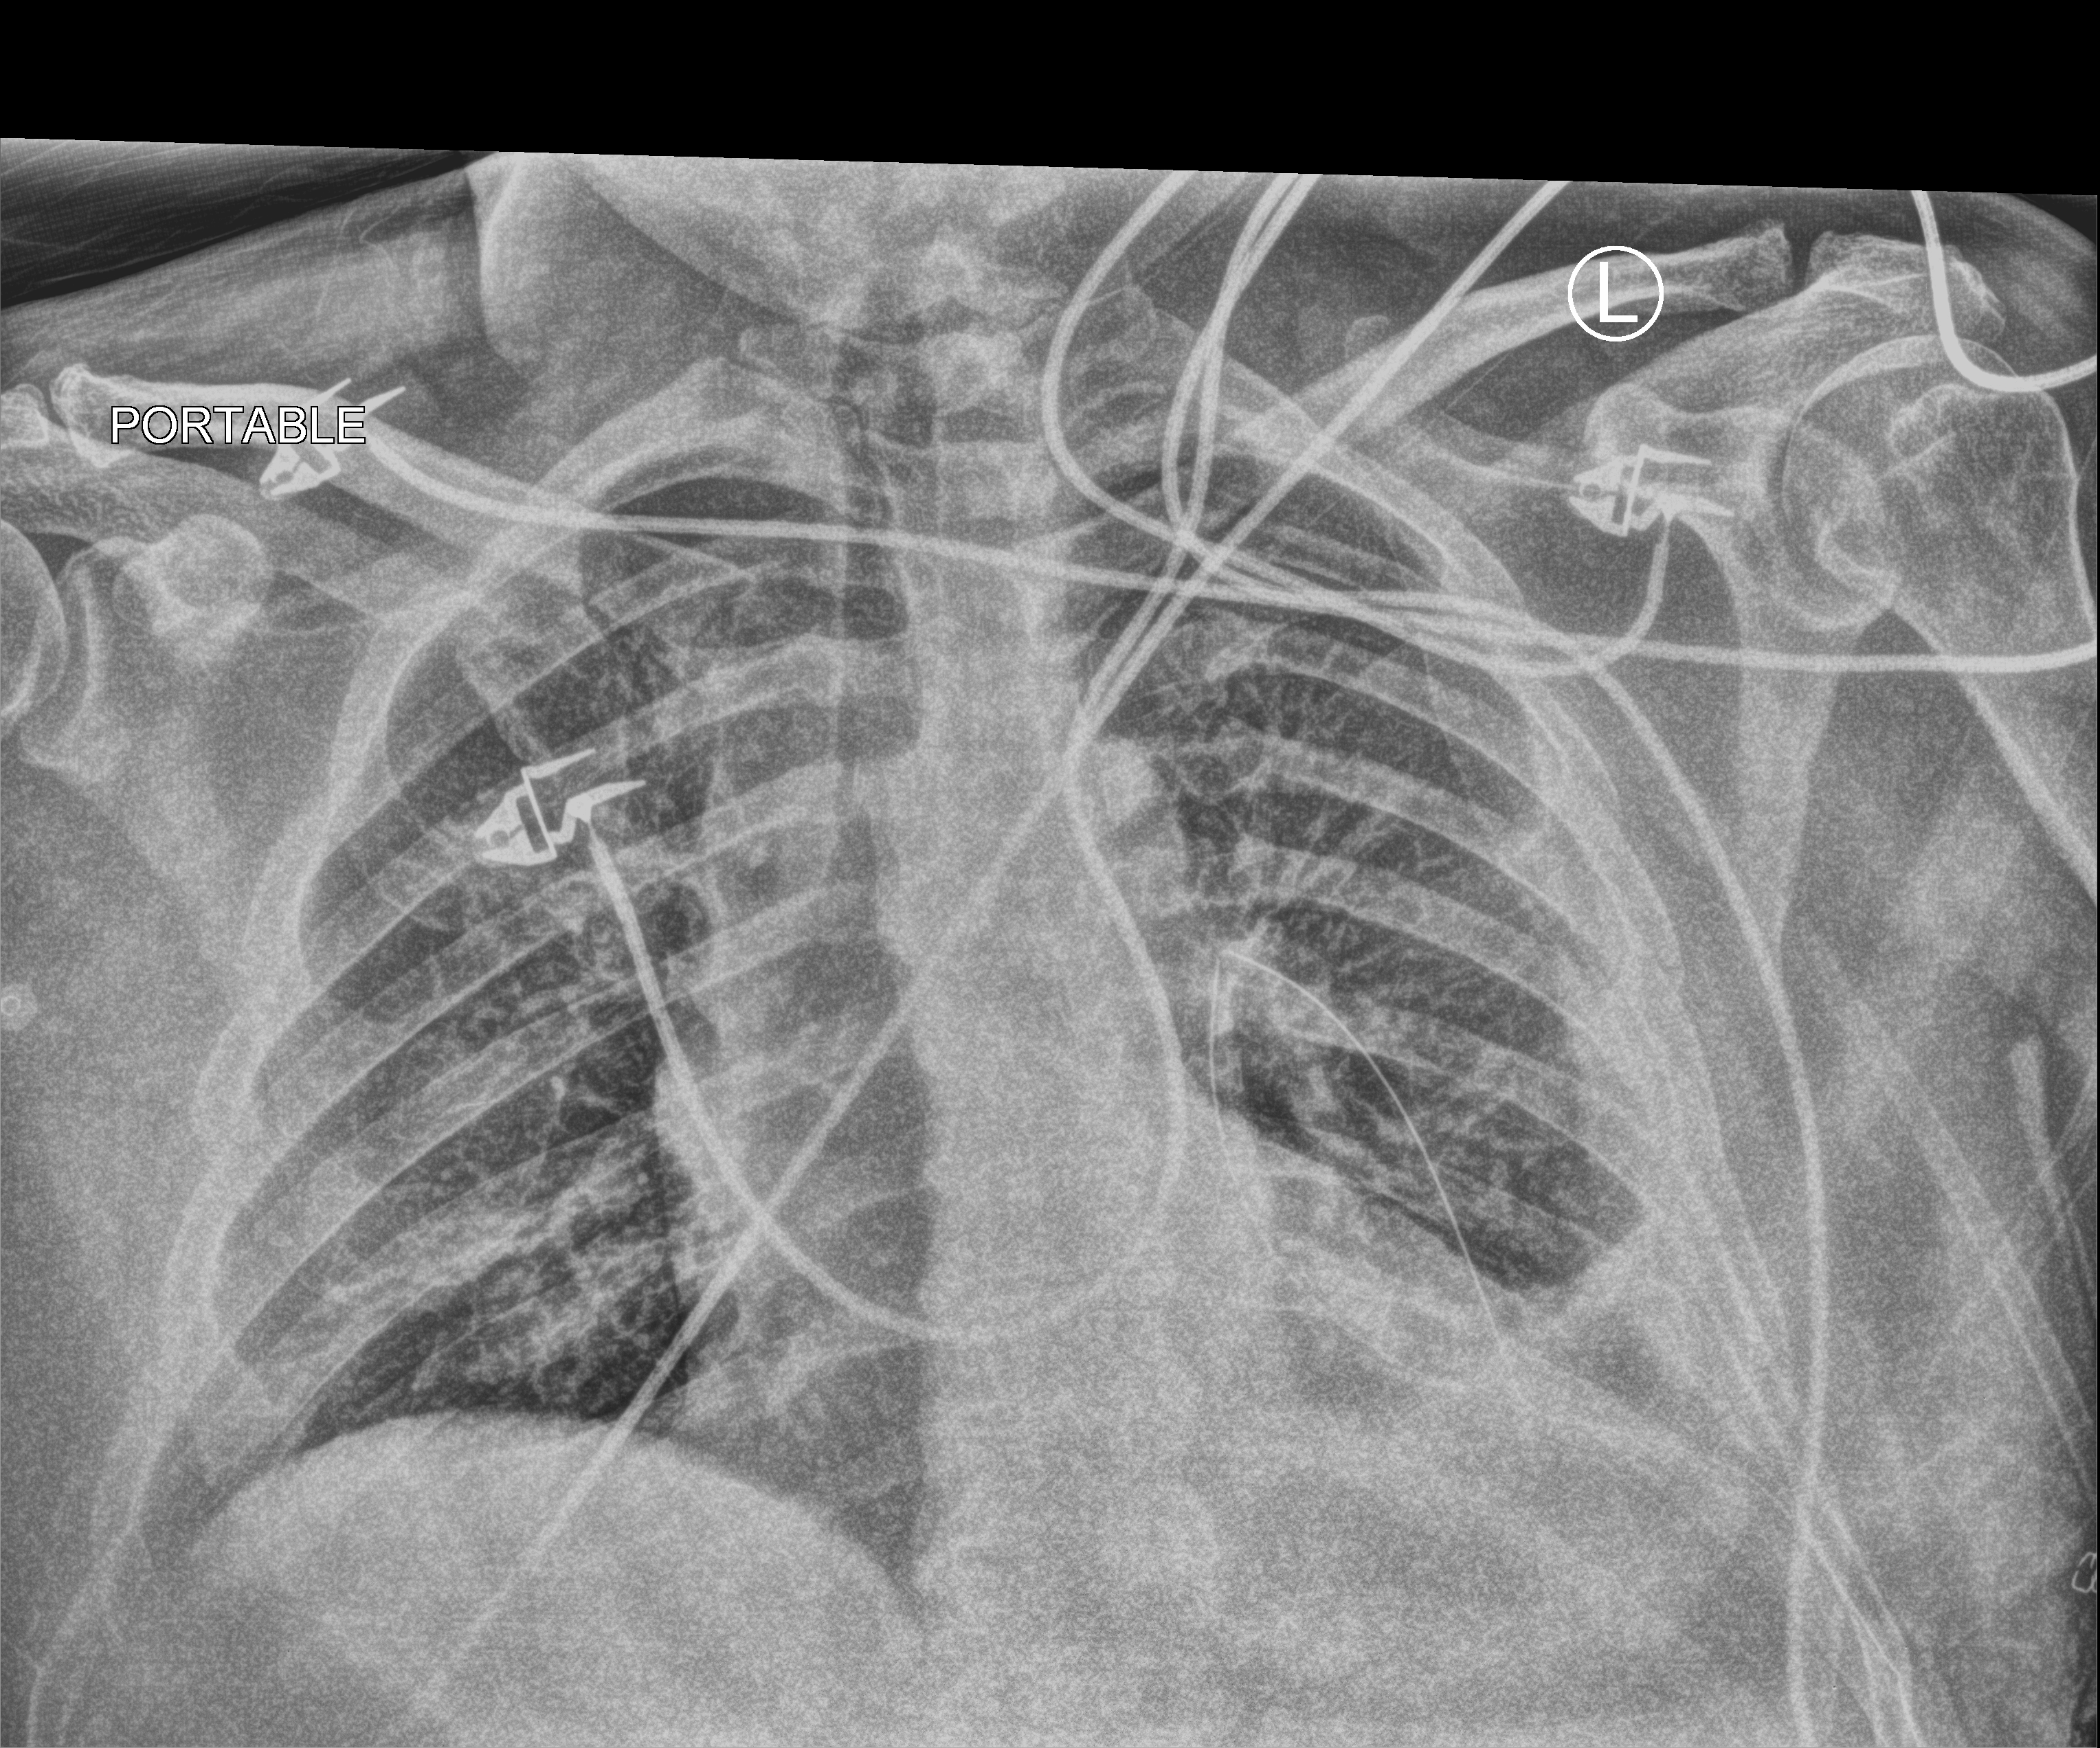
Chest X-ray (portable); anteroposterior (AP) projection. Male patient hospitalised with COVID-19, age 18–59 years.
From the hospital-stay record, not from the radiograph (when in the stay this image was taken is not recorded): admitted to intensive care during this hospital stay: no.